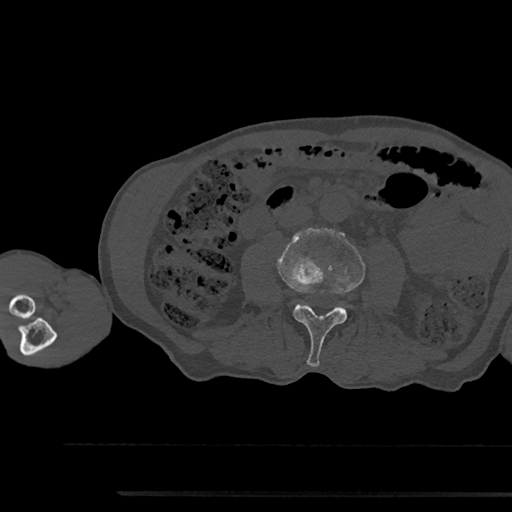
CT including the spine, one axial slice; slice 472 of 797 in the series (ordered by position); 120 kVp; bone window (W 1800 / L 400 HU); 512 × 512 image matrix. Patient: male, 79 years. Case-level facts recorded for this patient, not image findings: primary cancer: prostate.
Structures marked on this image (semi-automatically segmented with operator editing):
- L3 vertebra: box from (x=278, y=228) to (x=365, y=367) px